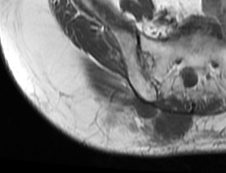
MRI of an extremity soft-tissue mass, one axial slice. Slice 53 of 73 in the series (ordered by position). MR volume resampled by the dataset authors to the PET/CT grid (not the native acquisition matrix). 3.27 mm slice thickness. 226 × 173 image matrix. Female patient. From the clinical record (not read from this slice): histological type: spindle cell suggestive of myxofibrosarcoma; grade: intermediate; site of the primary tumour: right buttock.
Outlined on this slice (expert contour drawn on MRI and transferred to this co-registered scan by the dataset authors):
- gross tumour volume (mass): bounding box [x1, y1, x2, y2] px = [91, 94, 190, 144]